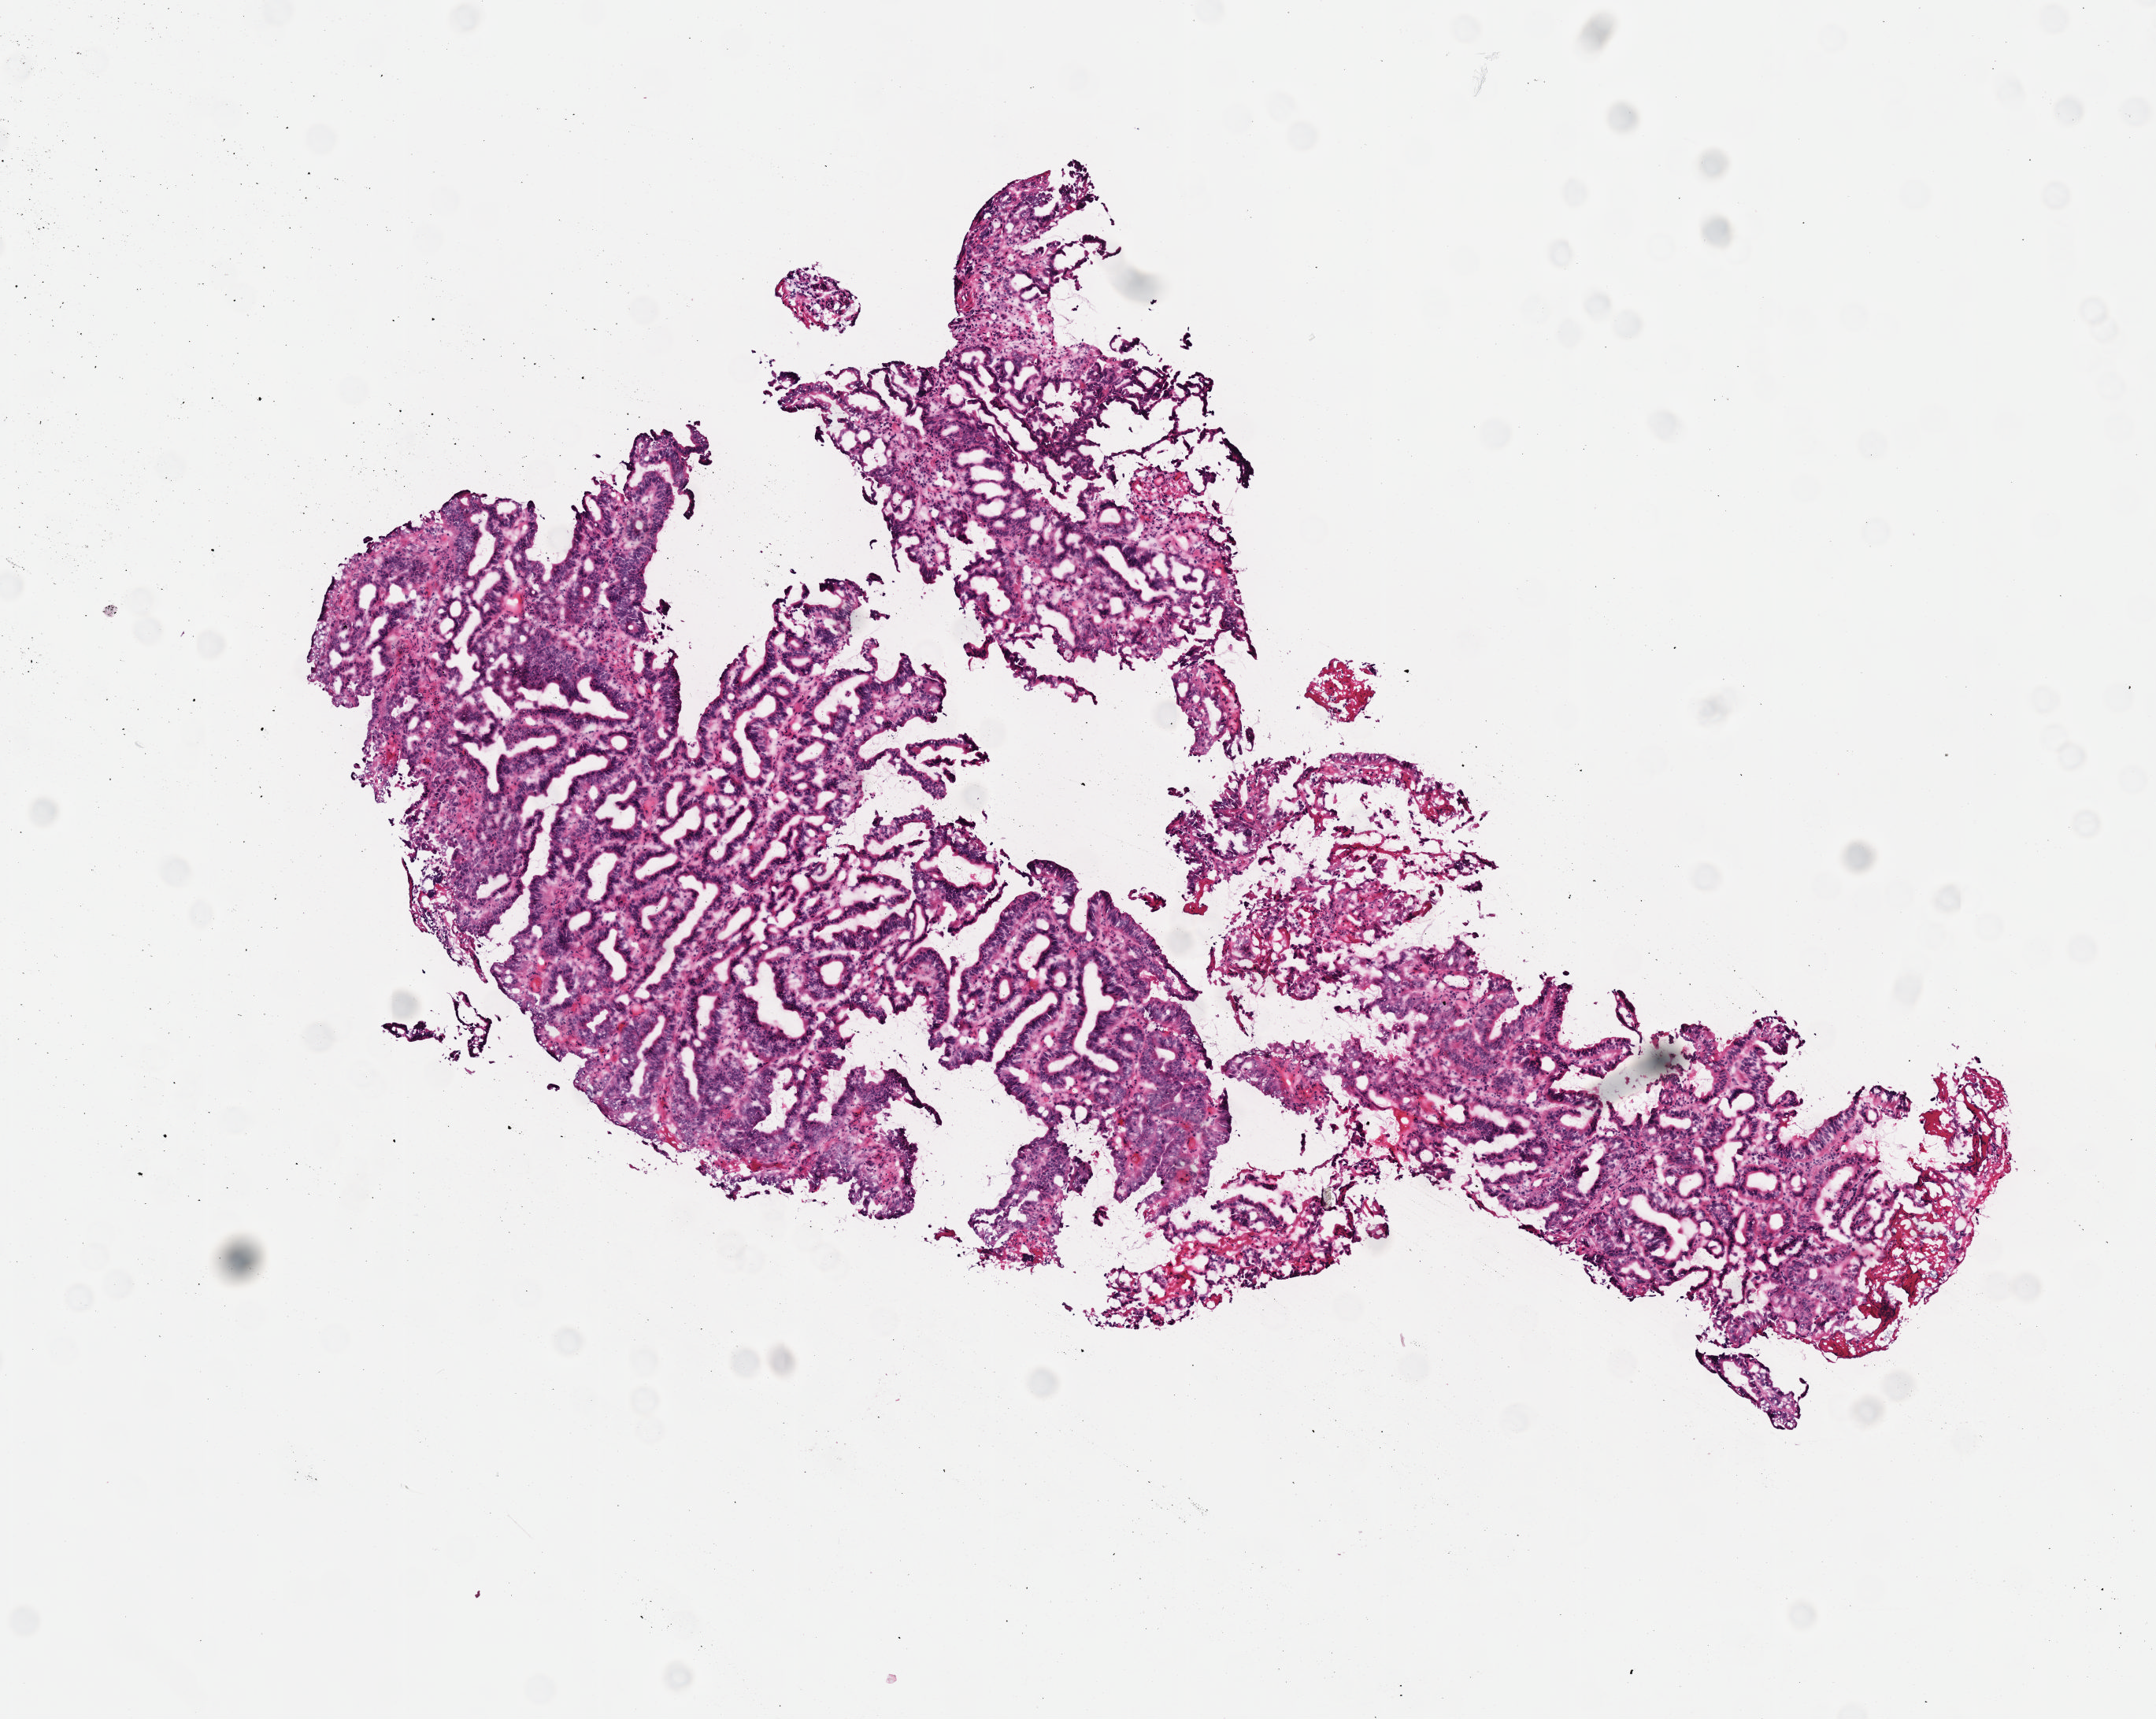
H&E-stained whole-slide image — low-resolution overview of the scanned area, about 5.5 x 4.4 mm; frozen section from the top of the tissue portion; esophagus, primary tumour sample. Male, age 72 years at initial diagnosis. Histologic grade: G3 (poorly differentiated). Pathologist review of this section (percent, as recorded): tumour cells 70%, tumour nuclei 70%, normal cells 0%, stromal cells 30%, necrosis 0%. Inflammatory infiltration, as recorded: lymphocyte infiltration 40%, monocyte infiltration 20%, neutrophil infiltration 20%.
Diagnosis: Adenocarcinoma, NOS.